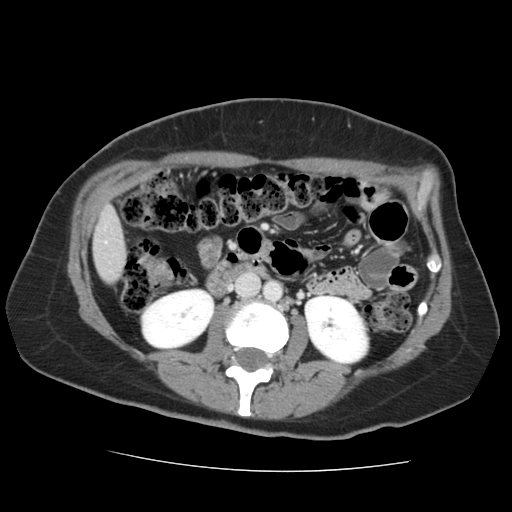
Contrast-enhanced abdominal CT, one axial slice. Position 46 of 144 along the scan axis. 120 kVp. Soft-tissue window (W 400 / L 40 HU). 2.5 mm slice thickness. 512 × 512 image matrix, field of view 333 × 333 mm. Female patient, age 46 years. Case-level facts recorded for this patient, not image findings: diagnosis: colorectal cancer liver metastases, imaged before liver resection; multiple liver metastases: no; largest metastasis: 2.8 cm; chemotherapy before resection: yes.
Outlined on this slice (manually delineated by an expert):
- liver: box from (x=94, y=210) to (x=126, y=283) px
- planned liver remnant (the part of the liver to remain after resection): (x=96, y=210)–(x=119, y=231)